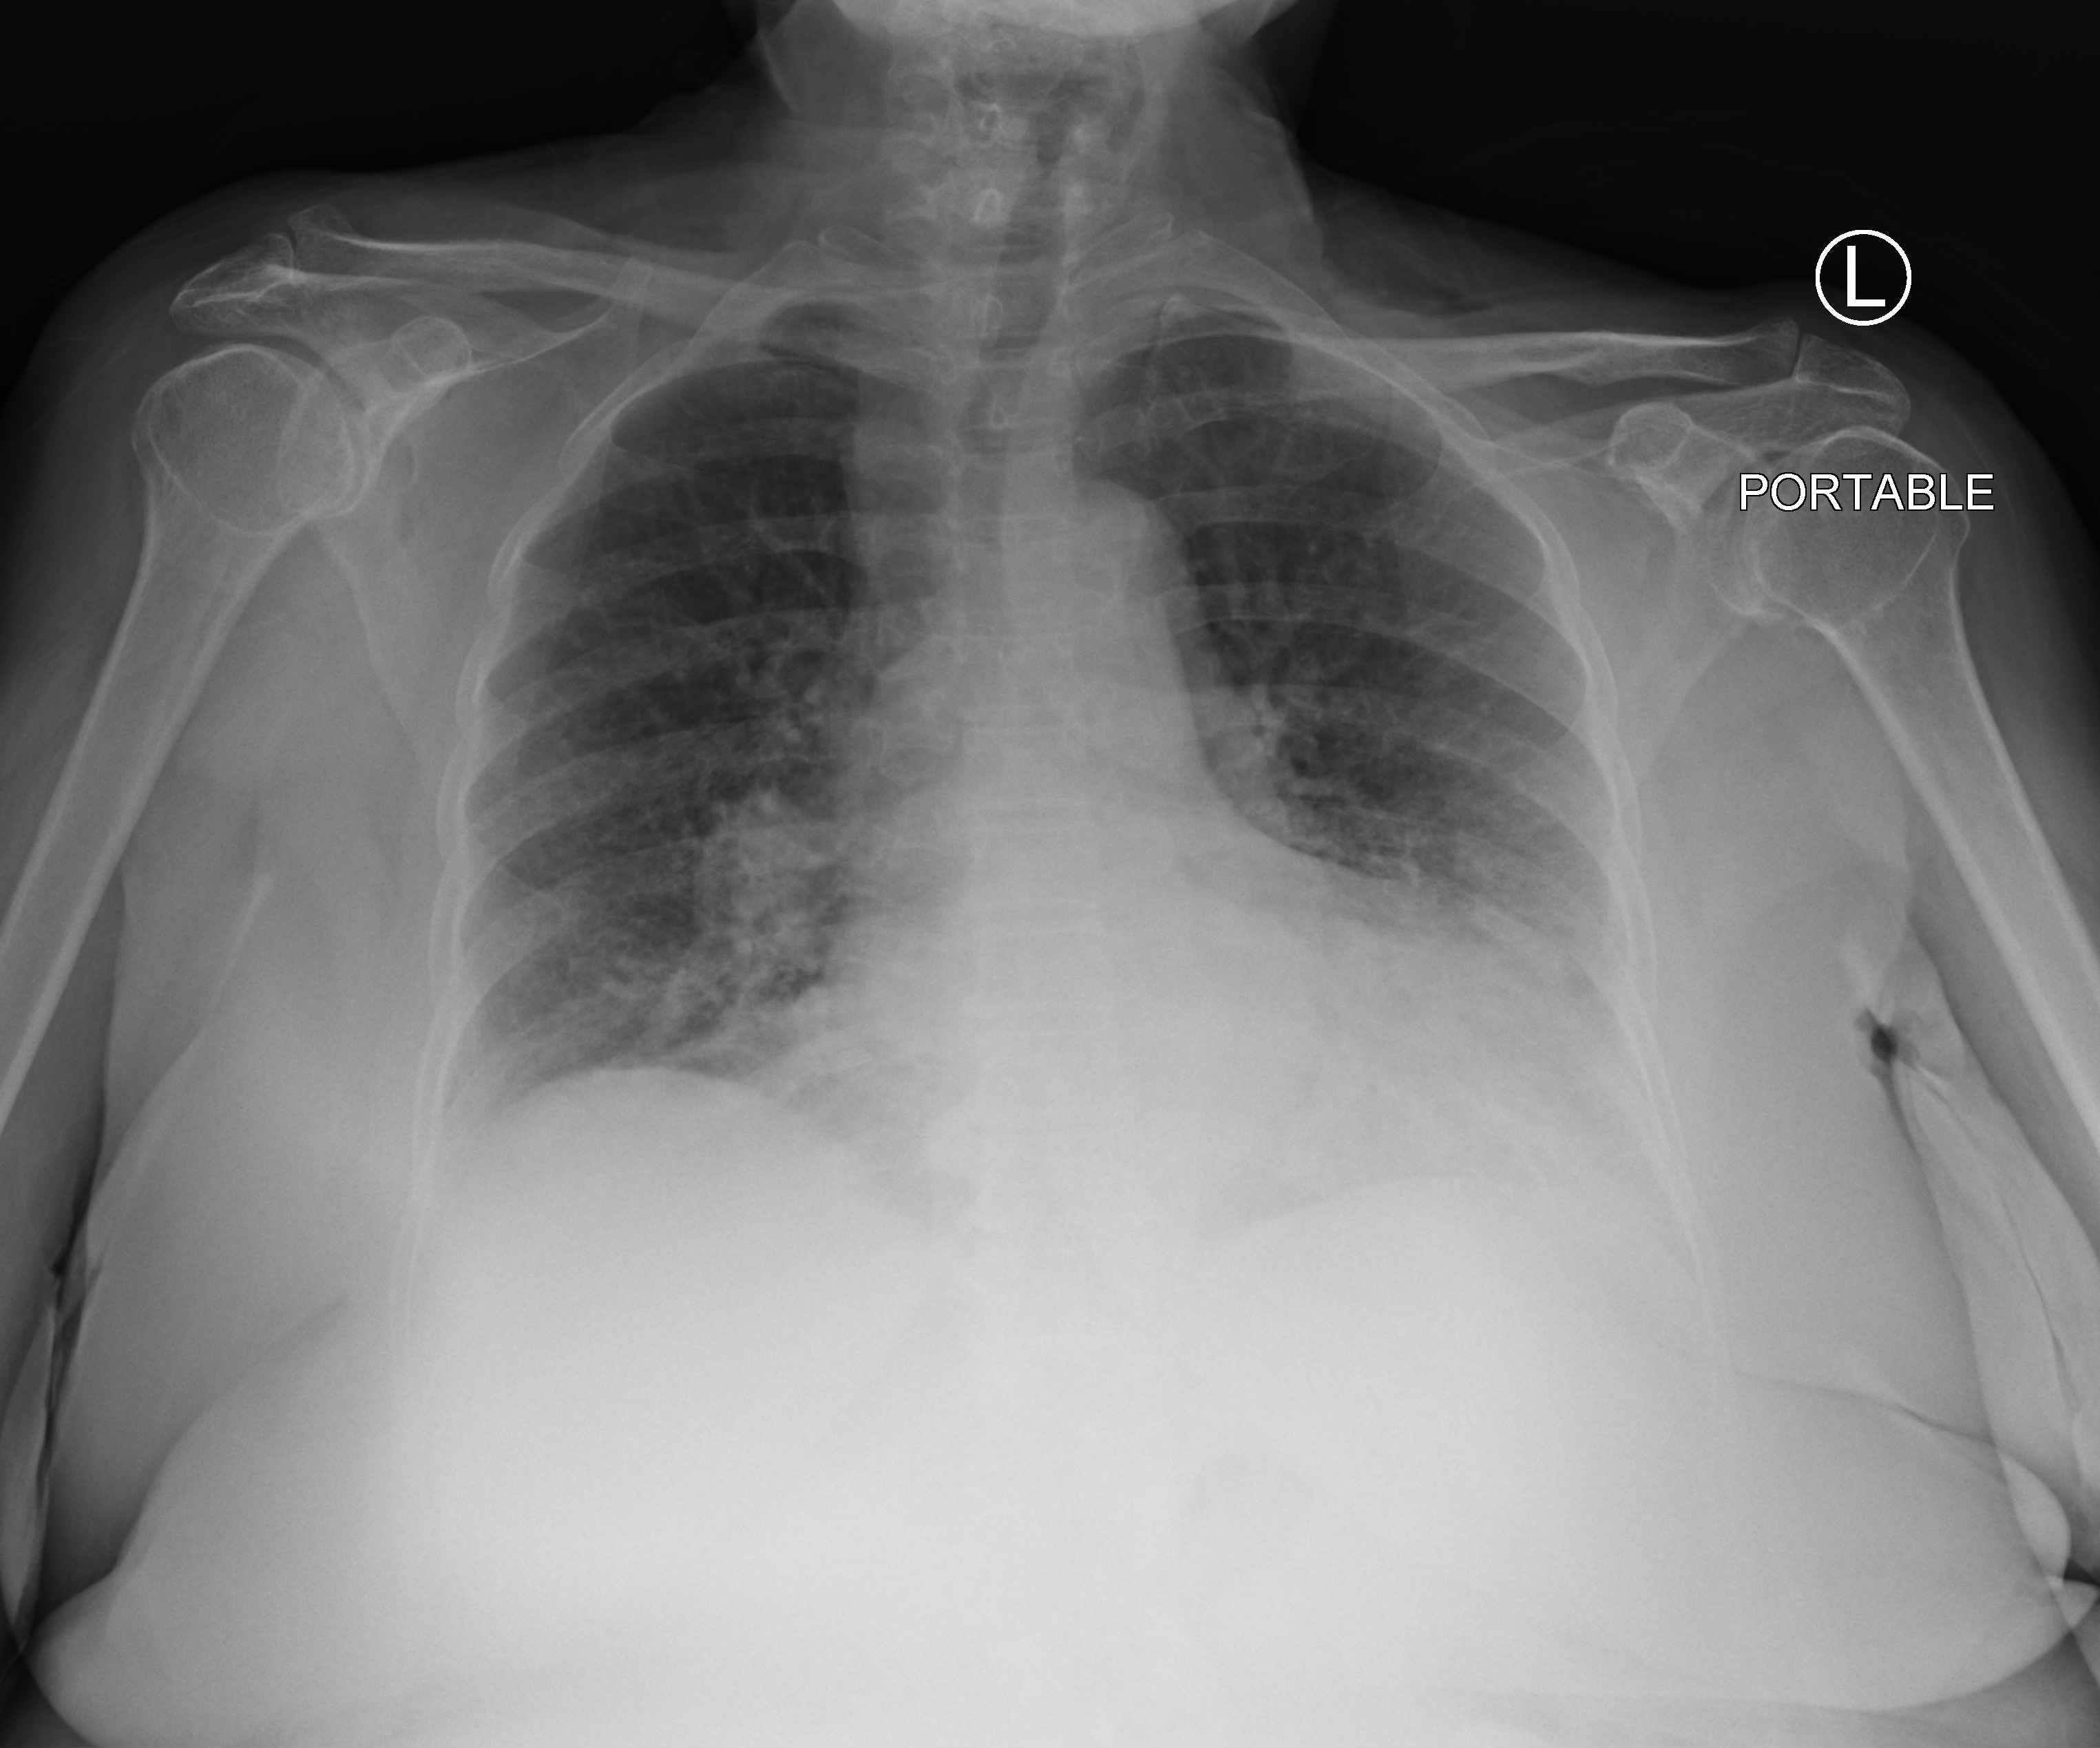
Portable chest radiograph. Patient hospitalised with COVID-19; female, aged 75–90 years.
Admission-level facts for this patient (not findings on this image; timing relative to this image not recorded):
- mechanically ventilated during this hospital stay: no
- length of hospital stay: 5 days
- admitted to intensive care during this hospital stay: no